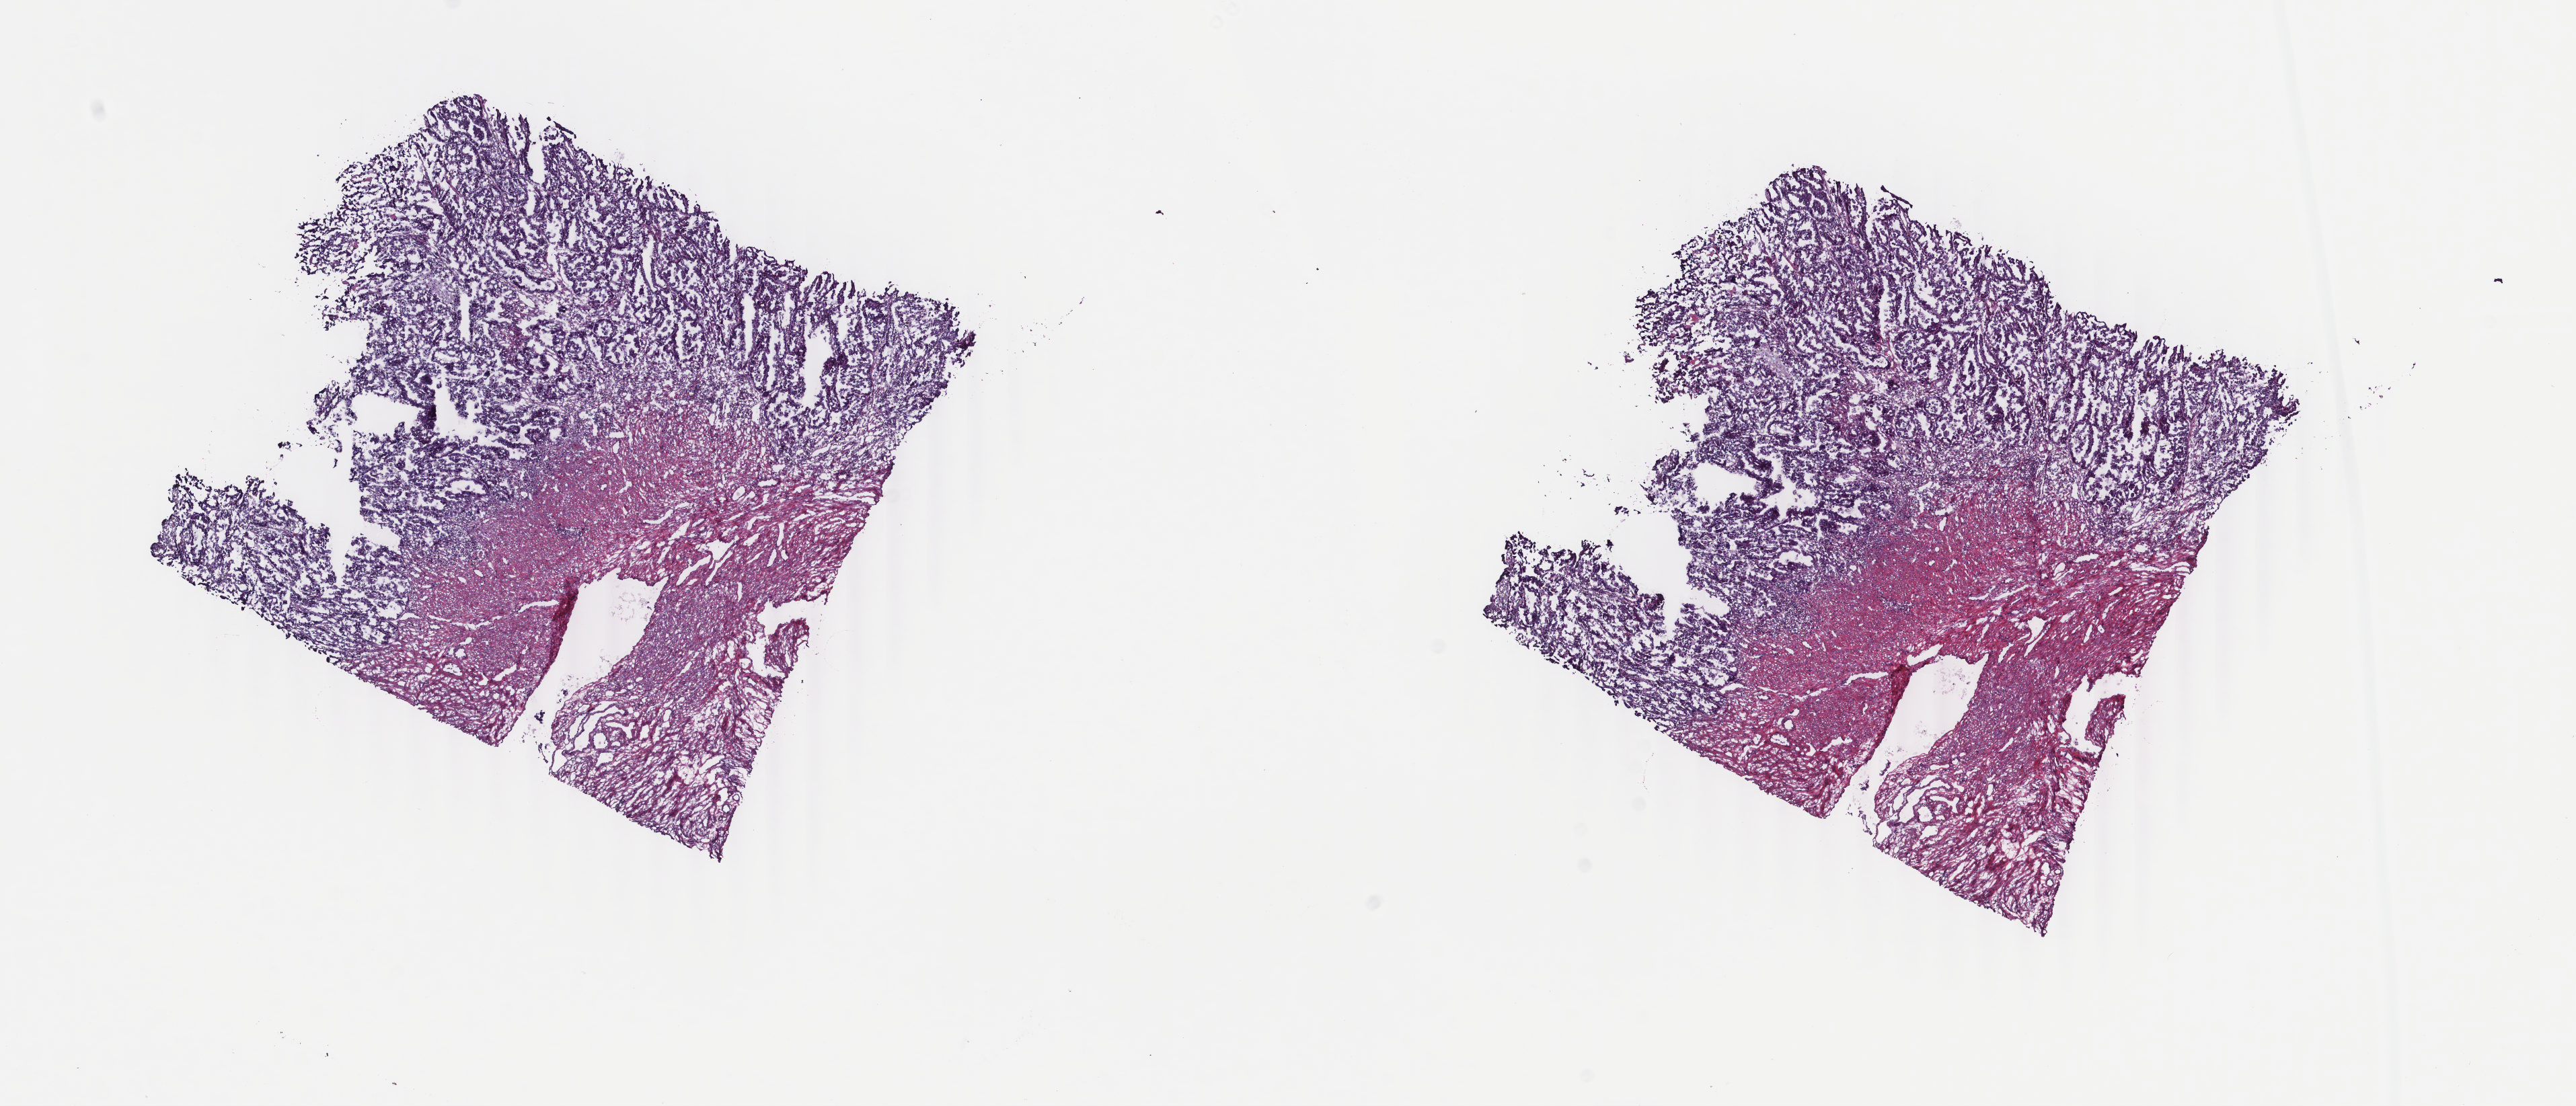
Hematoxylin and eosin (H&E) stained whole-slide image — whole scanned area (about 15.2 x 6.5 mm, from a 40x scan) shown as a low-resolution overview. Frozen section from the top of the tissue portion. Sample: primary tumour, uterus. Female patient; age at initial diagnosis 74 years. Histologic grade: G3 (poorly differentiated). Pathologist review of this section (percent, as recorded): tumour cells 65%, tumour nuclei 65%, normal cells 0%, stromal cells 25%, necrosis 10%. Infiltration values recorded for this section: lymphocyte infiltration 40%, monocyte infiltration 20%, neutrophil infiltration 20%.
- lymph nodes positive (case pathology): 0 of 37 examined
- FIGO stage: IA
- histologic diagnosis: Serous cystadenocarcinoma, NOS